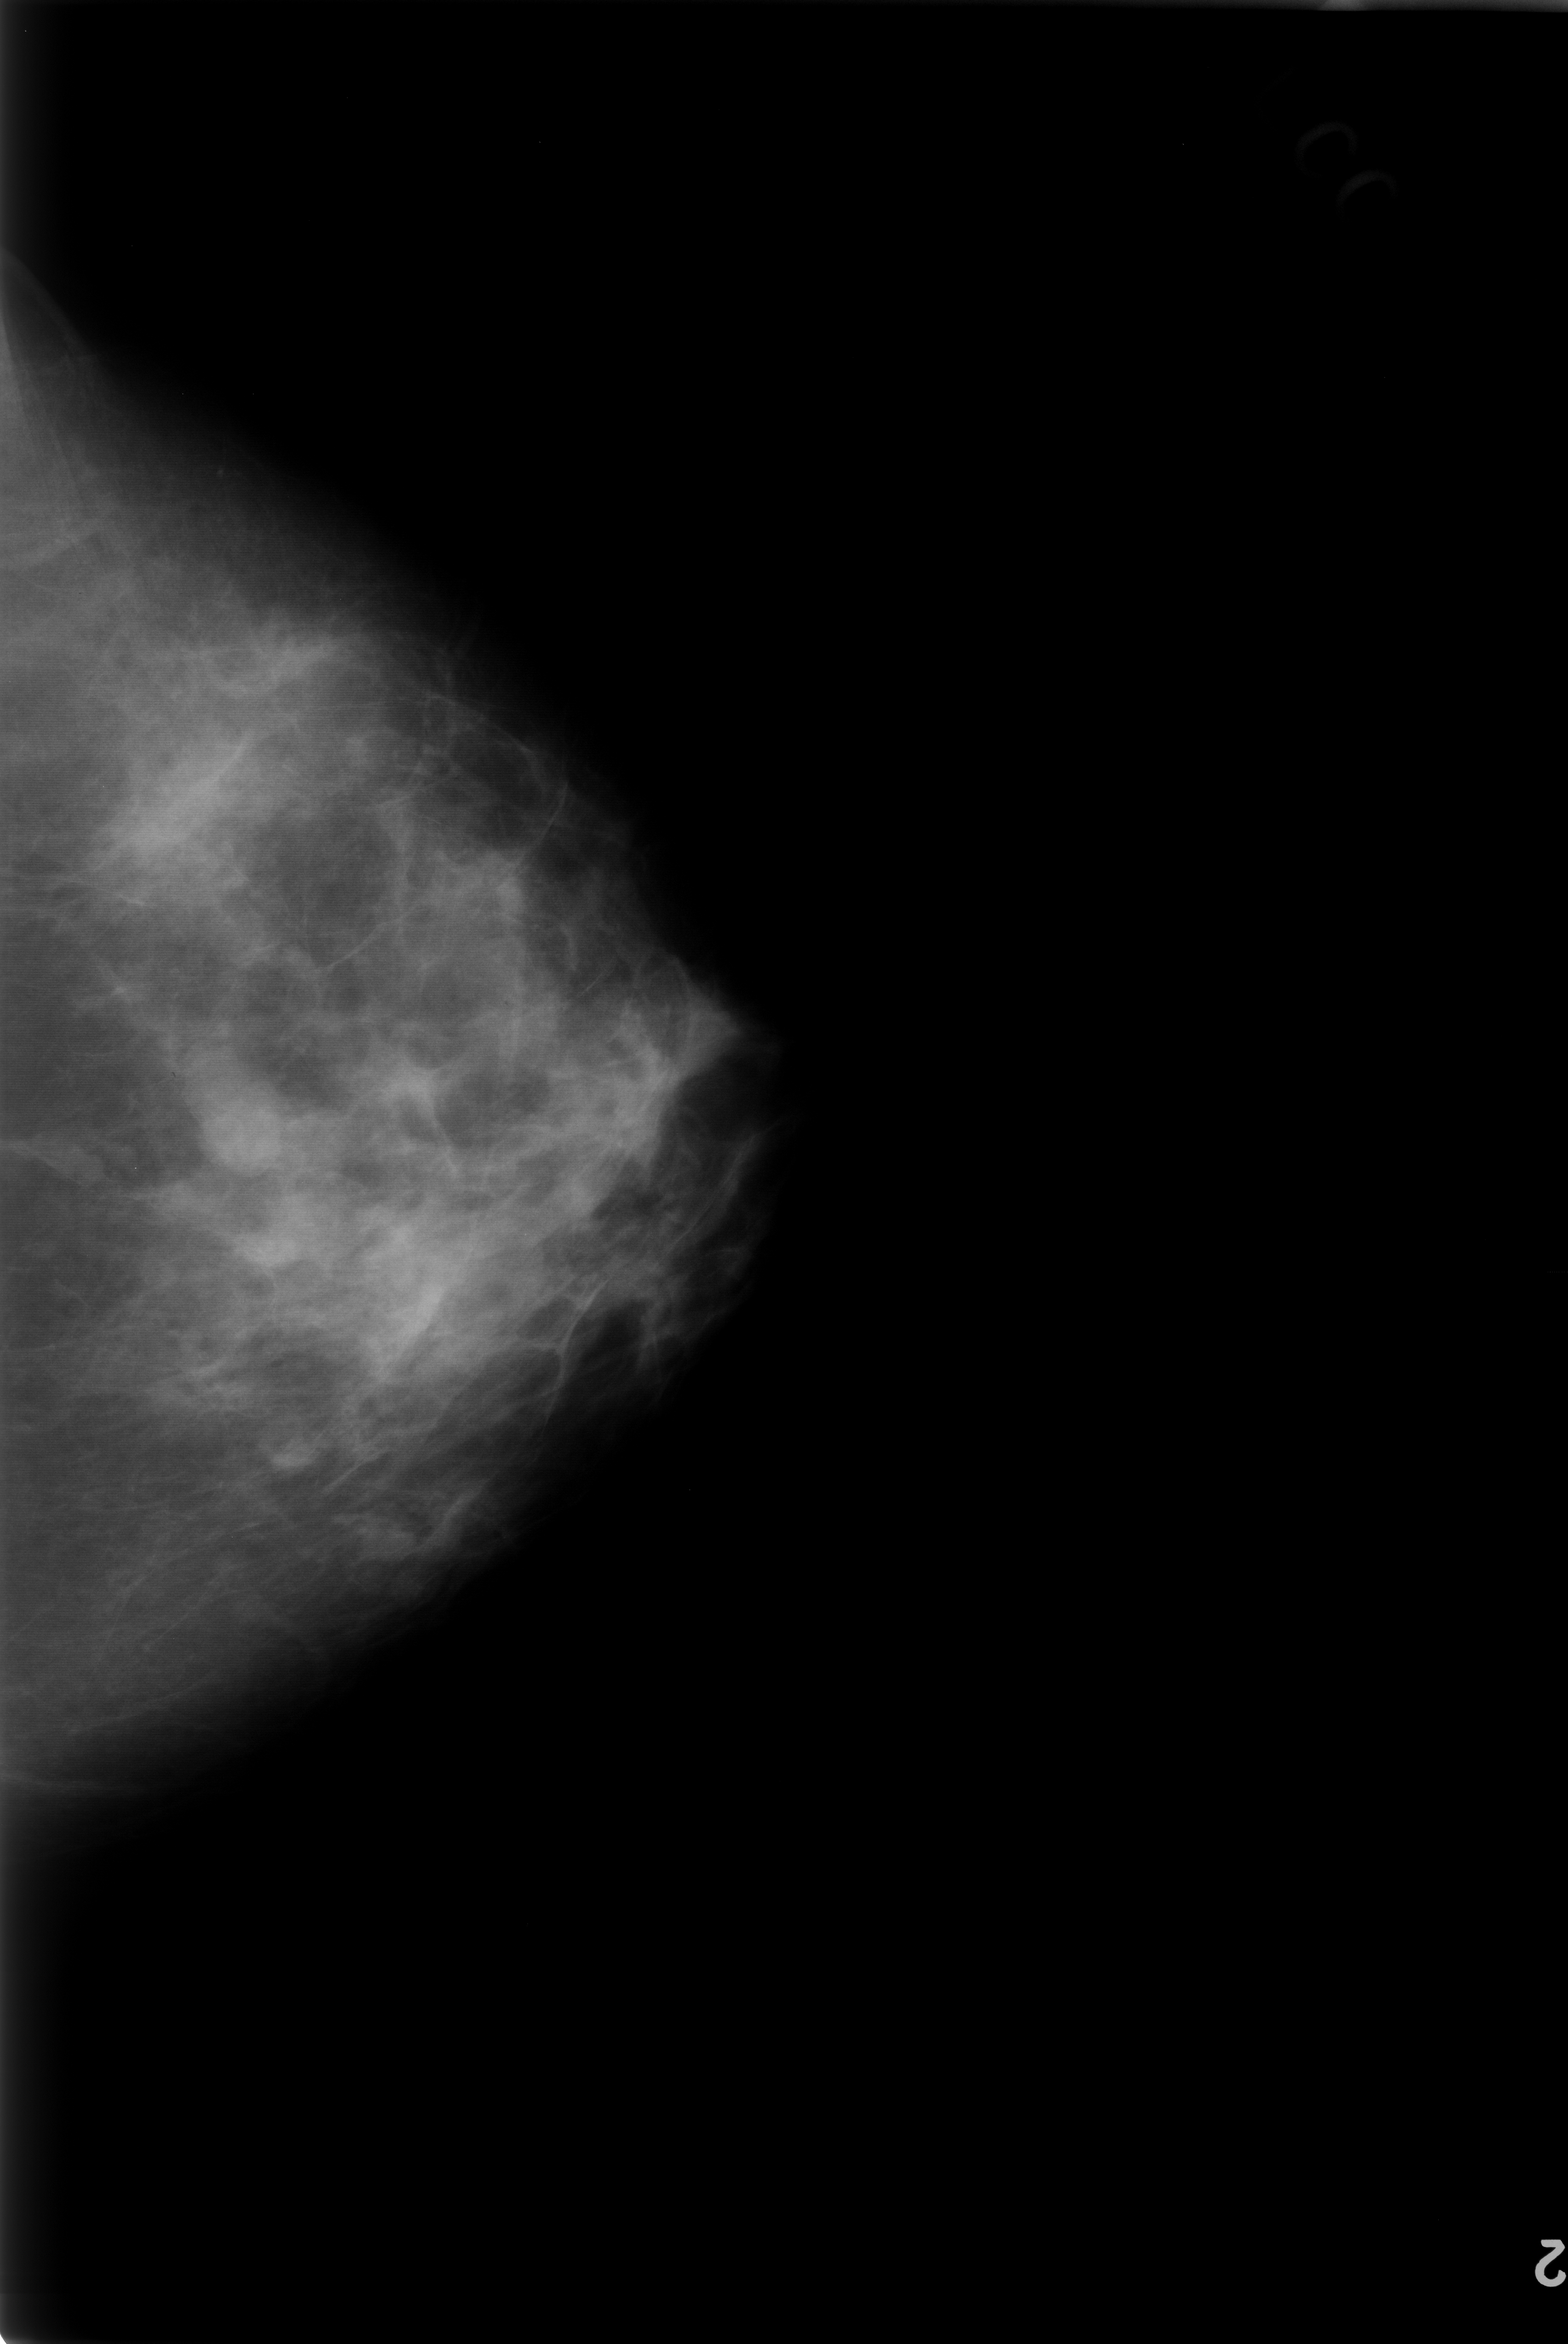
Mammogram (digitized film); left breast; CC view; BI-RADS breast density category 2 (scale 1–4); 1568 × 2344 image matrix.
Marked abnormalities (boxes around the expert regions of interest):
- mass, shape lobulated, margins circumscribed; BI-RADS assessment category 3; pathology (as recorded): benign: box from (x=187, y=1072) to (x=310, y=1173) px